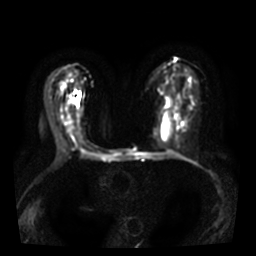
Breast MRI, one axial slice. Slice 18 of 38 in the series (ordered by position). Diffusion-weighted series; image 2 of 4 stored at this slice position (different b-values; order by instance number). 3 T. 256 × 256 image matrix. Female patient.
Structures marked on this image (outlined manually by an expert reader):
- tumour on diffusion-weighted imaging: bounding box (x1, y1, x2, y2) in pixels: (74, 94, 79, 103)